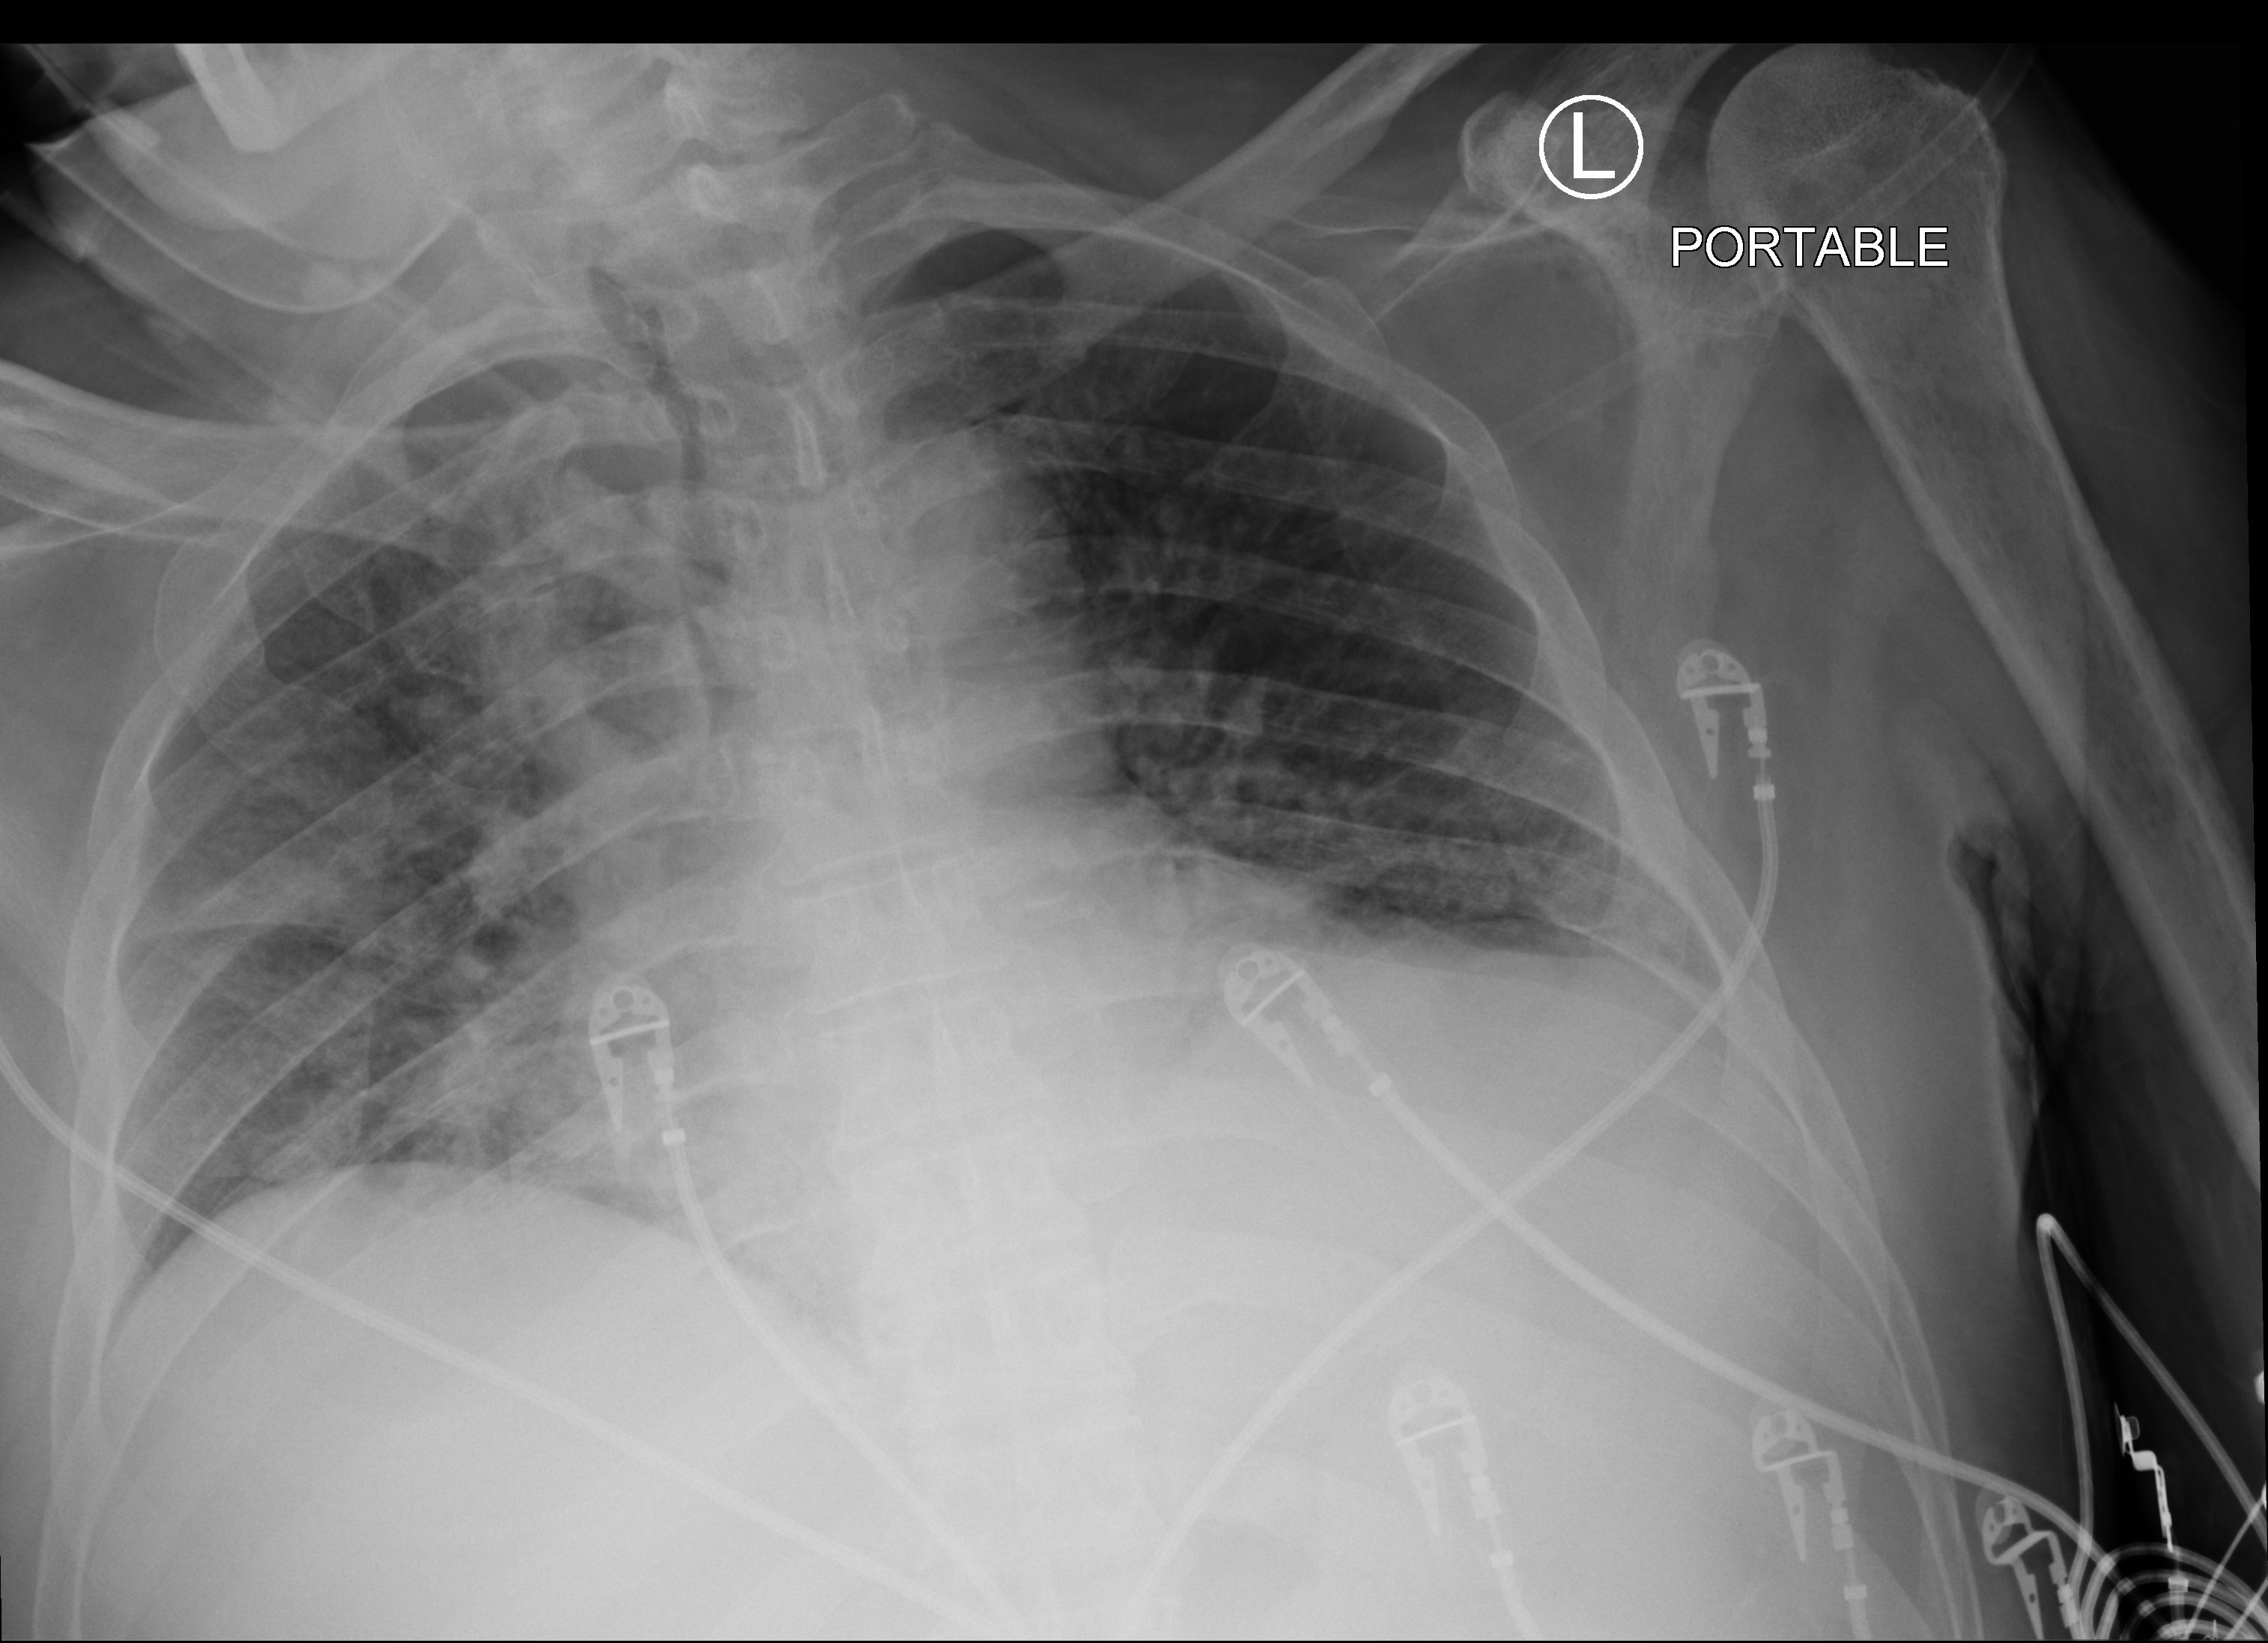
Portable chest radiograph, anteroposterior (AP) projection. Patient hospitalised with COVID-19; male, aged 60–74 years.
From the hospital-stay record, not from the radiograph (when in the stay this image was taken is not recorded):
- hypertension (admission record): yes